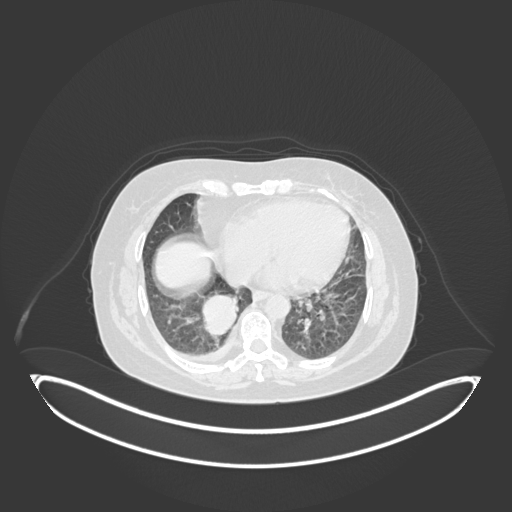
Chest CT, one axial slice; position 50 of 231 along the scan axis; reconstruction kernel B30f; 120 kVp; lung window (W 1500 / L -600 HU); 512 × 512 image matrix, field of view 500 × 500 mm. Female patient, age 56 years. Case-level facts recorded for this patient, not image findings: clinical TNM (as recorded): T2b N1 M0.
Annotated regions visible in this slice (rectangle marked by the reading radiologist):
- lung tumour (recorded histology: small cell carcinoma): box from (x=199, y=292) to (x=251, y=342) px